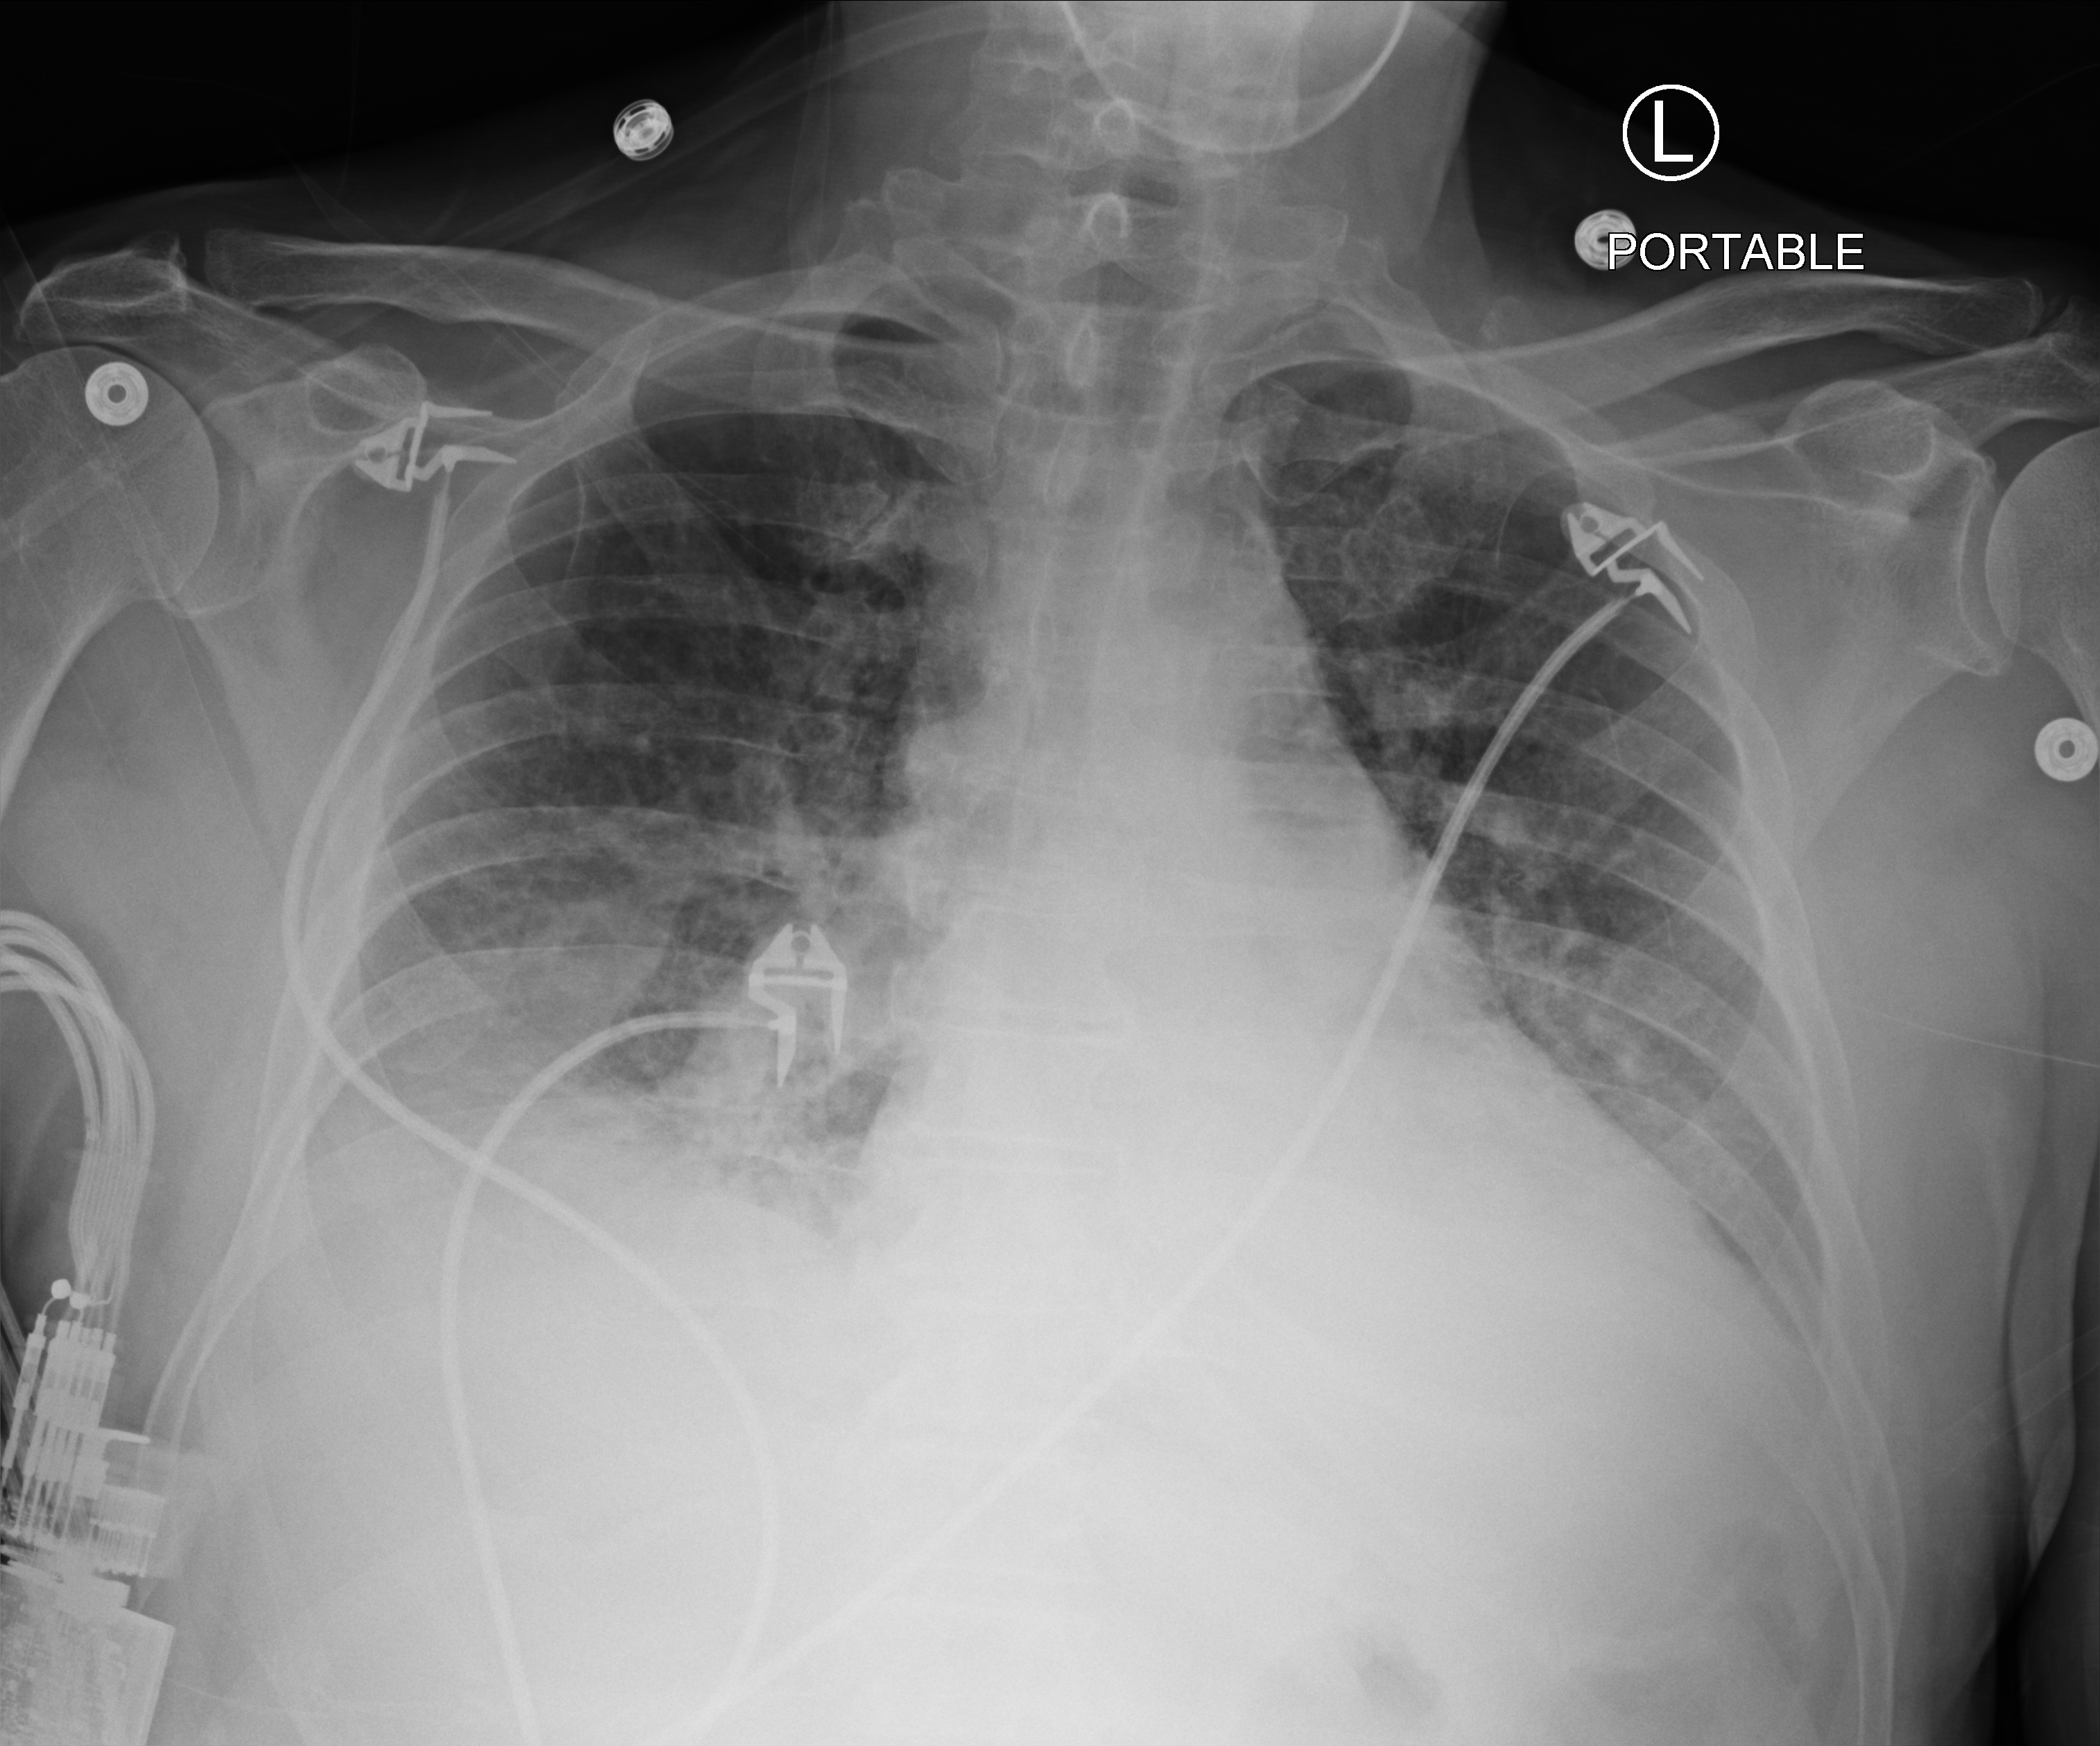
Chest X-ray (portable), anteroposterior (AP) projection. Male patient hospitalised with COVID-19, age 18–59 years.
Admission-level facts for this patient (not findings on this image; timing relative to this image not recorded): length of hospital stay: 16 days; mechanically ventilated during this hospital stay: no; admitted to intensive care during this hospital stay: no.